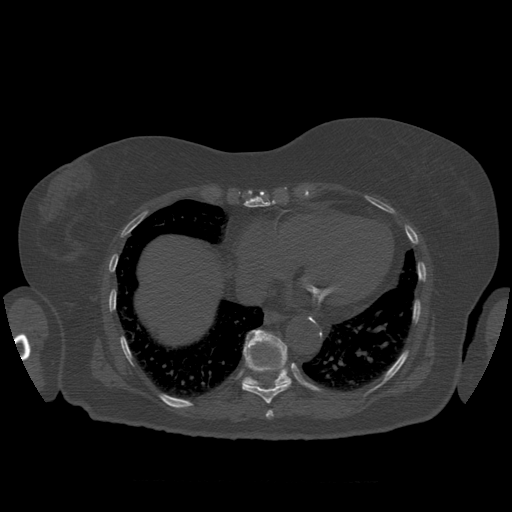
CT including the spine, one axial slice. Position 353 of 399 along the scan axis. Reconstruction kernel STANDARD. Bone window (W 1800 / L 400 HU). 1.25 mm slice thickness. 512 × 512 image matrix. Patient age 81 years. Case-level facts recorded for this patient, not image findings: primary cancer: renal.
Annotated regions visible in this slice (semi-automatically segmented with operator editing):
- T10 vertebra: box from (x=244, y=330) to (x=292, y=389) px
- T8 vertebra: (x=266, y=410)–(x=274, y=418)
- T9 vertebra: (x=242, y=333)–(x=290, y=404)